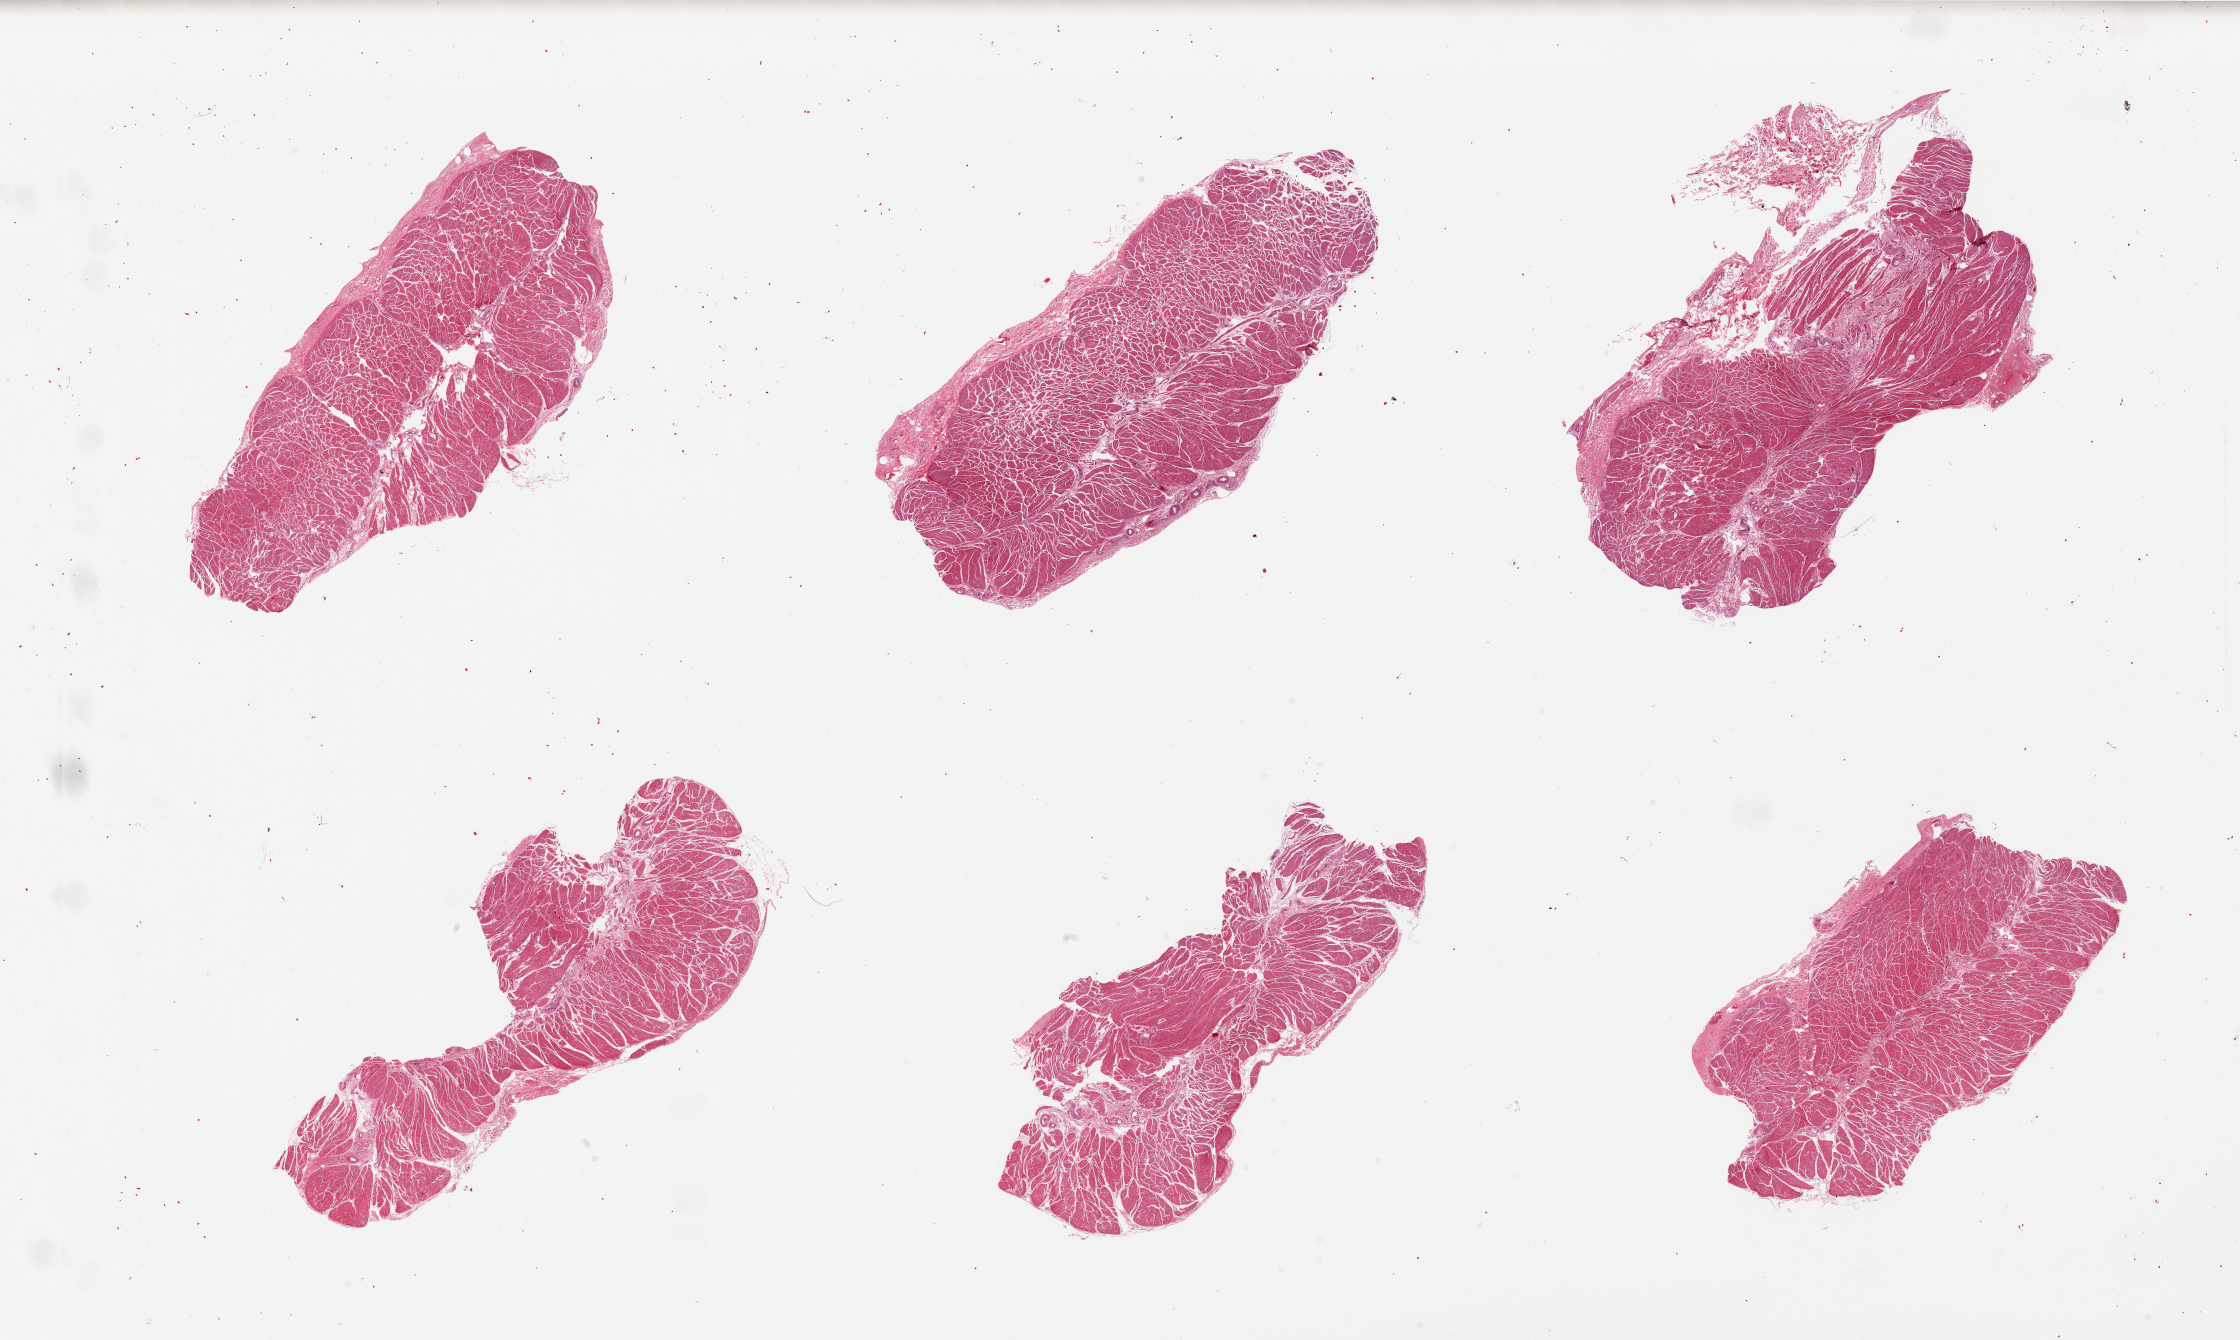
Digitized haematoxylin and eosin-stained section, whole scanned area (about 35.4 x 21.2 mm) shown as a low-resolution overview. PAXgene-fixed, paraffin-embedded tissue. Target tissue: esophageal muscle. Donor tissue sample. Male donor.
Review note (as recorded): 6 pieces. Well trimmed.